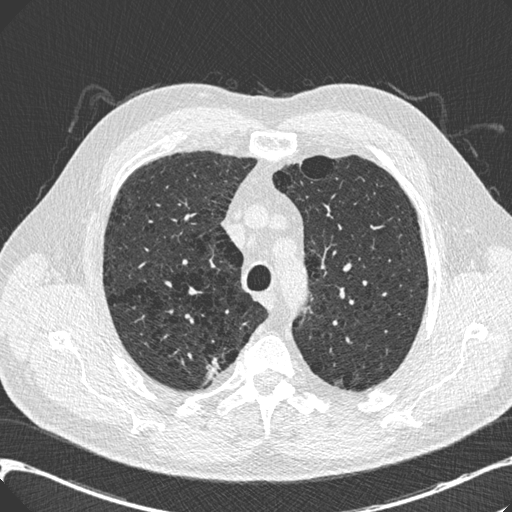
Low-dose screening chest CT, one axial slice. Slice 152 of 197 in the series (ordered by position). 120 kVp. Lung window (W 1500 / L -600 HU). 0.75 mm slice thickness. 512 × 512 image matrix, field of view 367 × 367 mm.
Outlined on this slice (outlined manually by an expert reader):
- lesion 1 (tumor, upper lobe of right lung): box from (x=206, y=358) to (x=219, y=383) px